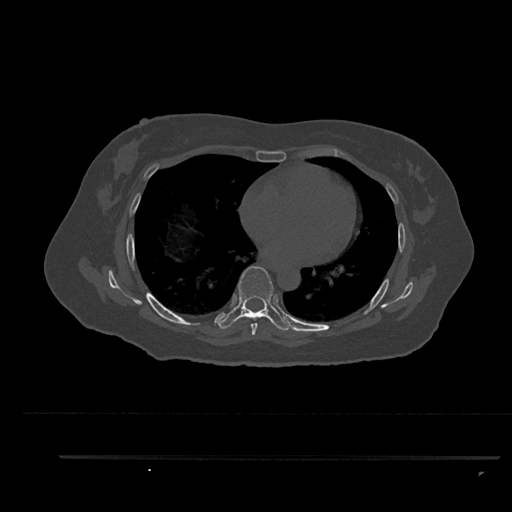
CT including the spine, one axial slice. Position 521 of 797 along the scan axis. Reconstruction kernel Br40s/3. Bone window (W 1800 / L 400 HU). 0.5 mm slice thickness. 512 × 512 image matrix, field of view 408 × 408 mm. Female patient, age 44 years. From the clinical record (not read from this slice): primary cancer: renal.
Annotated regions visible in this slice (semi-automatic segmentation, software-assisted and operator-edited):
- T6 vertebra: bounding box <250,318,258,335> (left, top, right, bottom; pixels)
- T7 vertebra: <218,266,293,331>